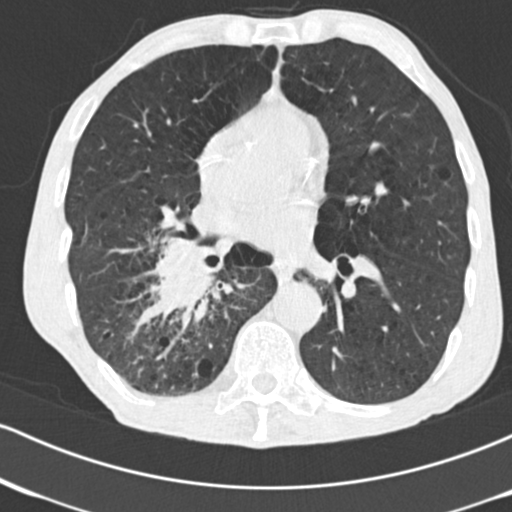
Low-dose screening chest CT, one axial slice; slice 80 of 182 in the series (ordered by position); reconstruction kernel B30f; lung window (W 1500 / L -600 HU); 512 × 512 image matrix, field of view 316 × 316 mm.
Outlined on this slice (outlined manually by an expert reader):
- lesion 1 (tumor, lower lobe of right lung): box from (x=151, y=242) to (x=218, y=313) px